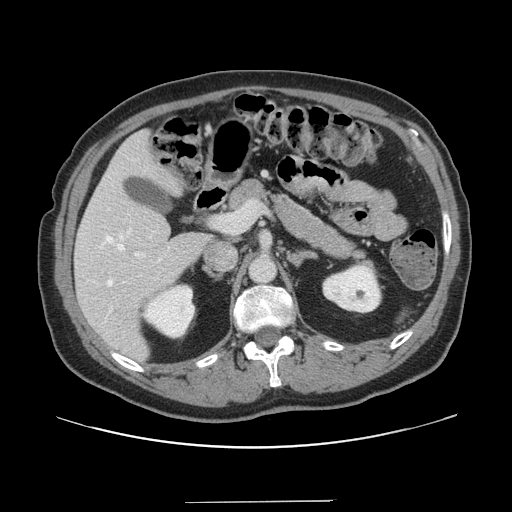
Contrast-enhanced abdominal CT, one axial slice. Slice 82 of 151 in the series (ordered by position). 120 kVp. Soft-tissue window (W 400 / L 40 HU). 512 × 512 image matrix, field of view 399 × 399 mm. Male patient, age 63 years. Case-level facts recorded for this patient, not image findings: diagnosis: colorectal cancer liver metastases, imaged before liver resection; multiple liver metastases: no; largest metastasis: 2.1 cm.
Outlined on this slice (expert manual segmentation):
- hepatic veins: bounding box <106,235,124,286> (left, top, right, bottom; pixels)
- liver: <76,132,211,361>
- planned liver remnant (the part of the liver to remain after resection): <76,132,211,361>
- portal vein (with intrahepatic branches): <134,201,257,258>